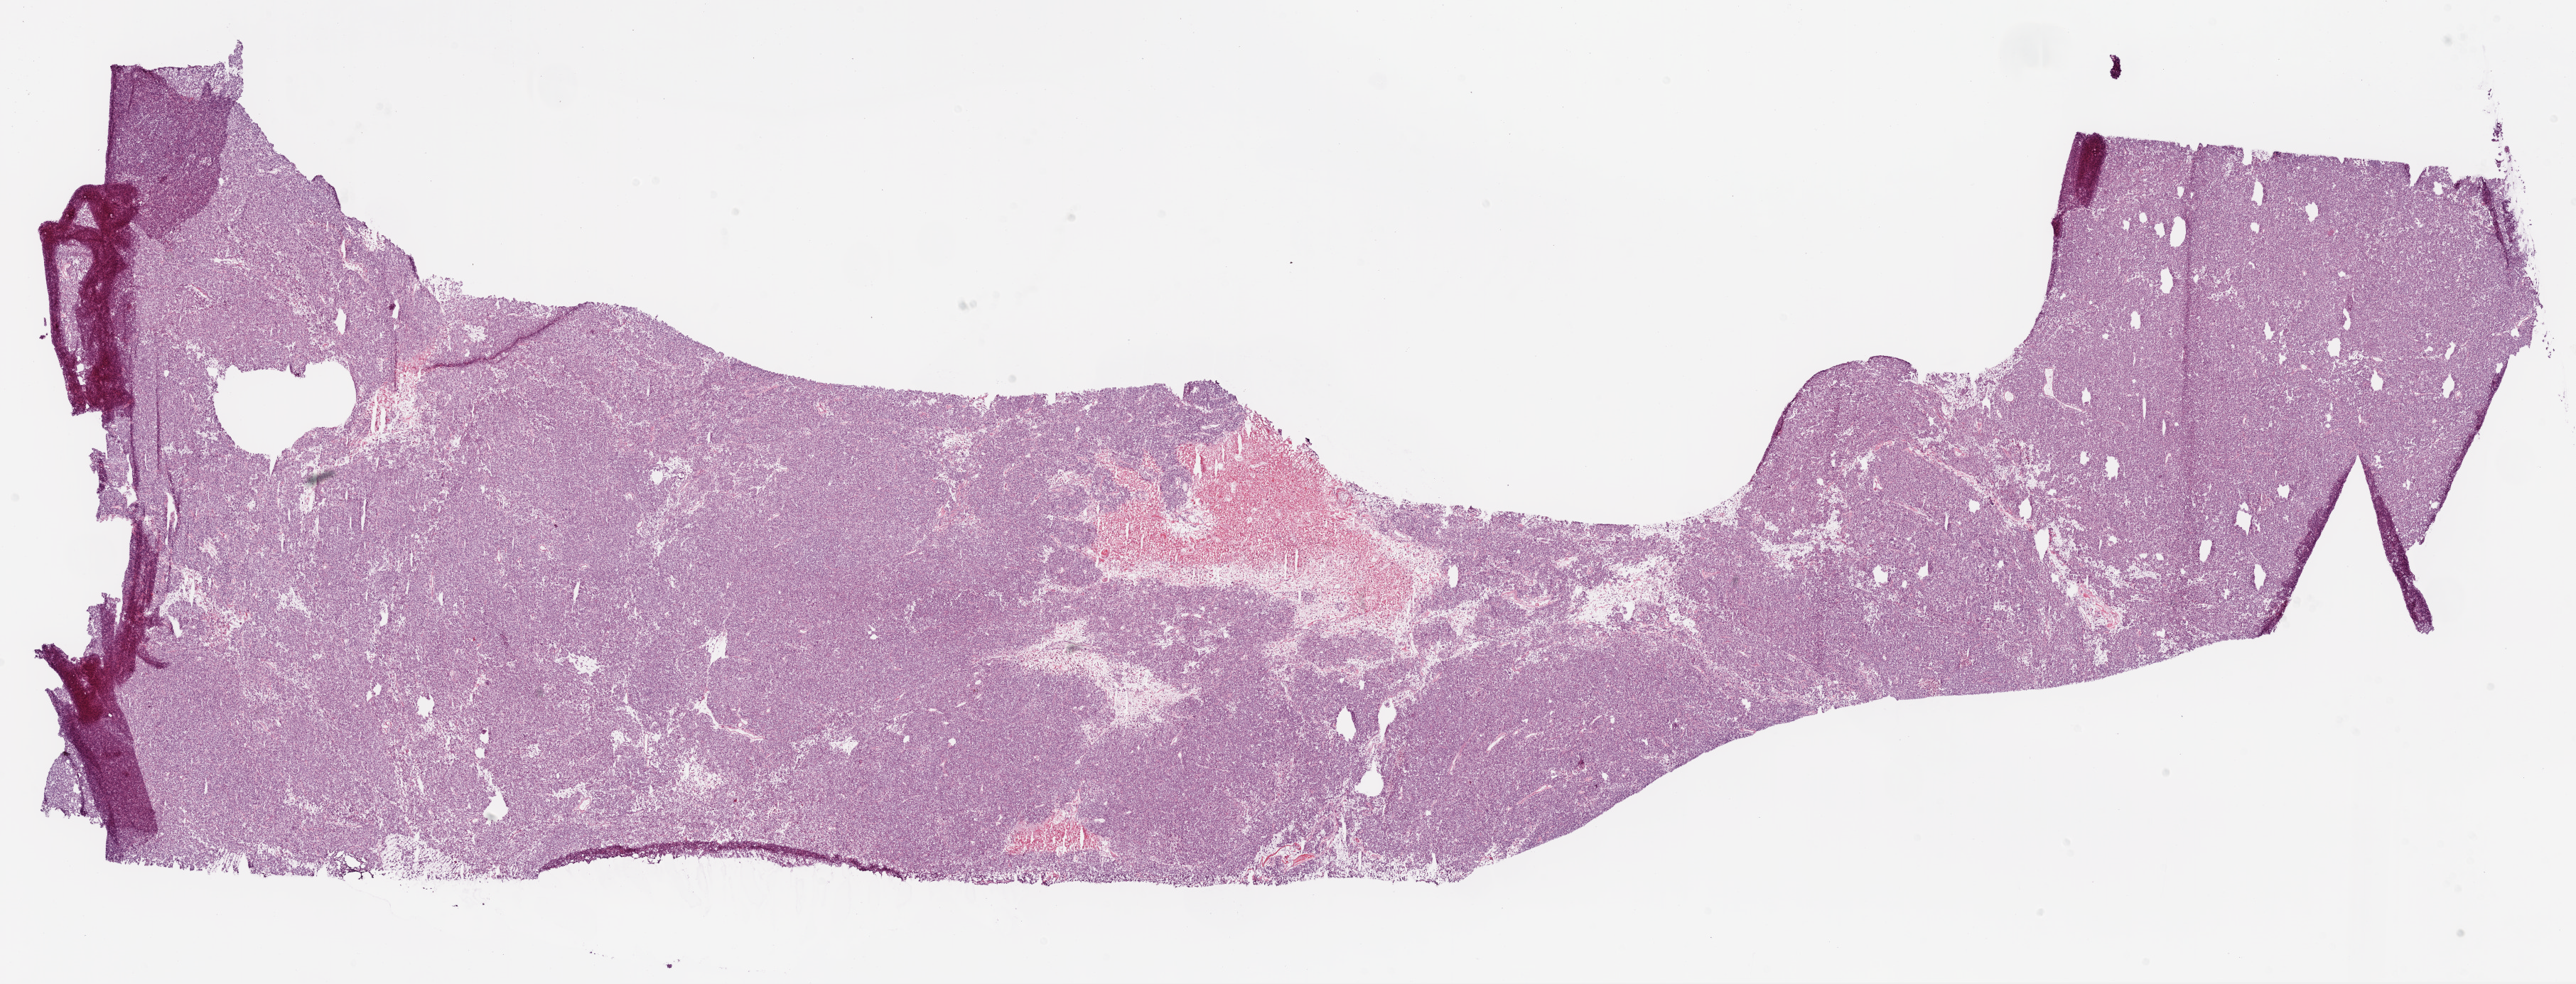
Digitized Hematoxylin and eosin (H&E) stained tissue section (whole slide), low-resolution overview of the scanned area, about 29.1 x 11.1 mm, frozen section, sample: primary tumour, ovary. Female patient; age at initial diagnosis 50 years. Histologic grade: G3 (poorly differentiated). Composition of this section per pathologist review: tumour cells 87%, tumour nuclei 99%, normal cells 0%, stromal cells 5%, necrosis 8%.
* FIGO stage: IV
* diagnosis: Serous cystadenocarcinoma, NOS